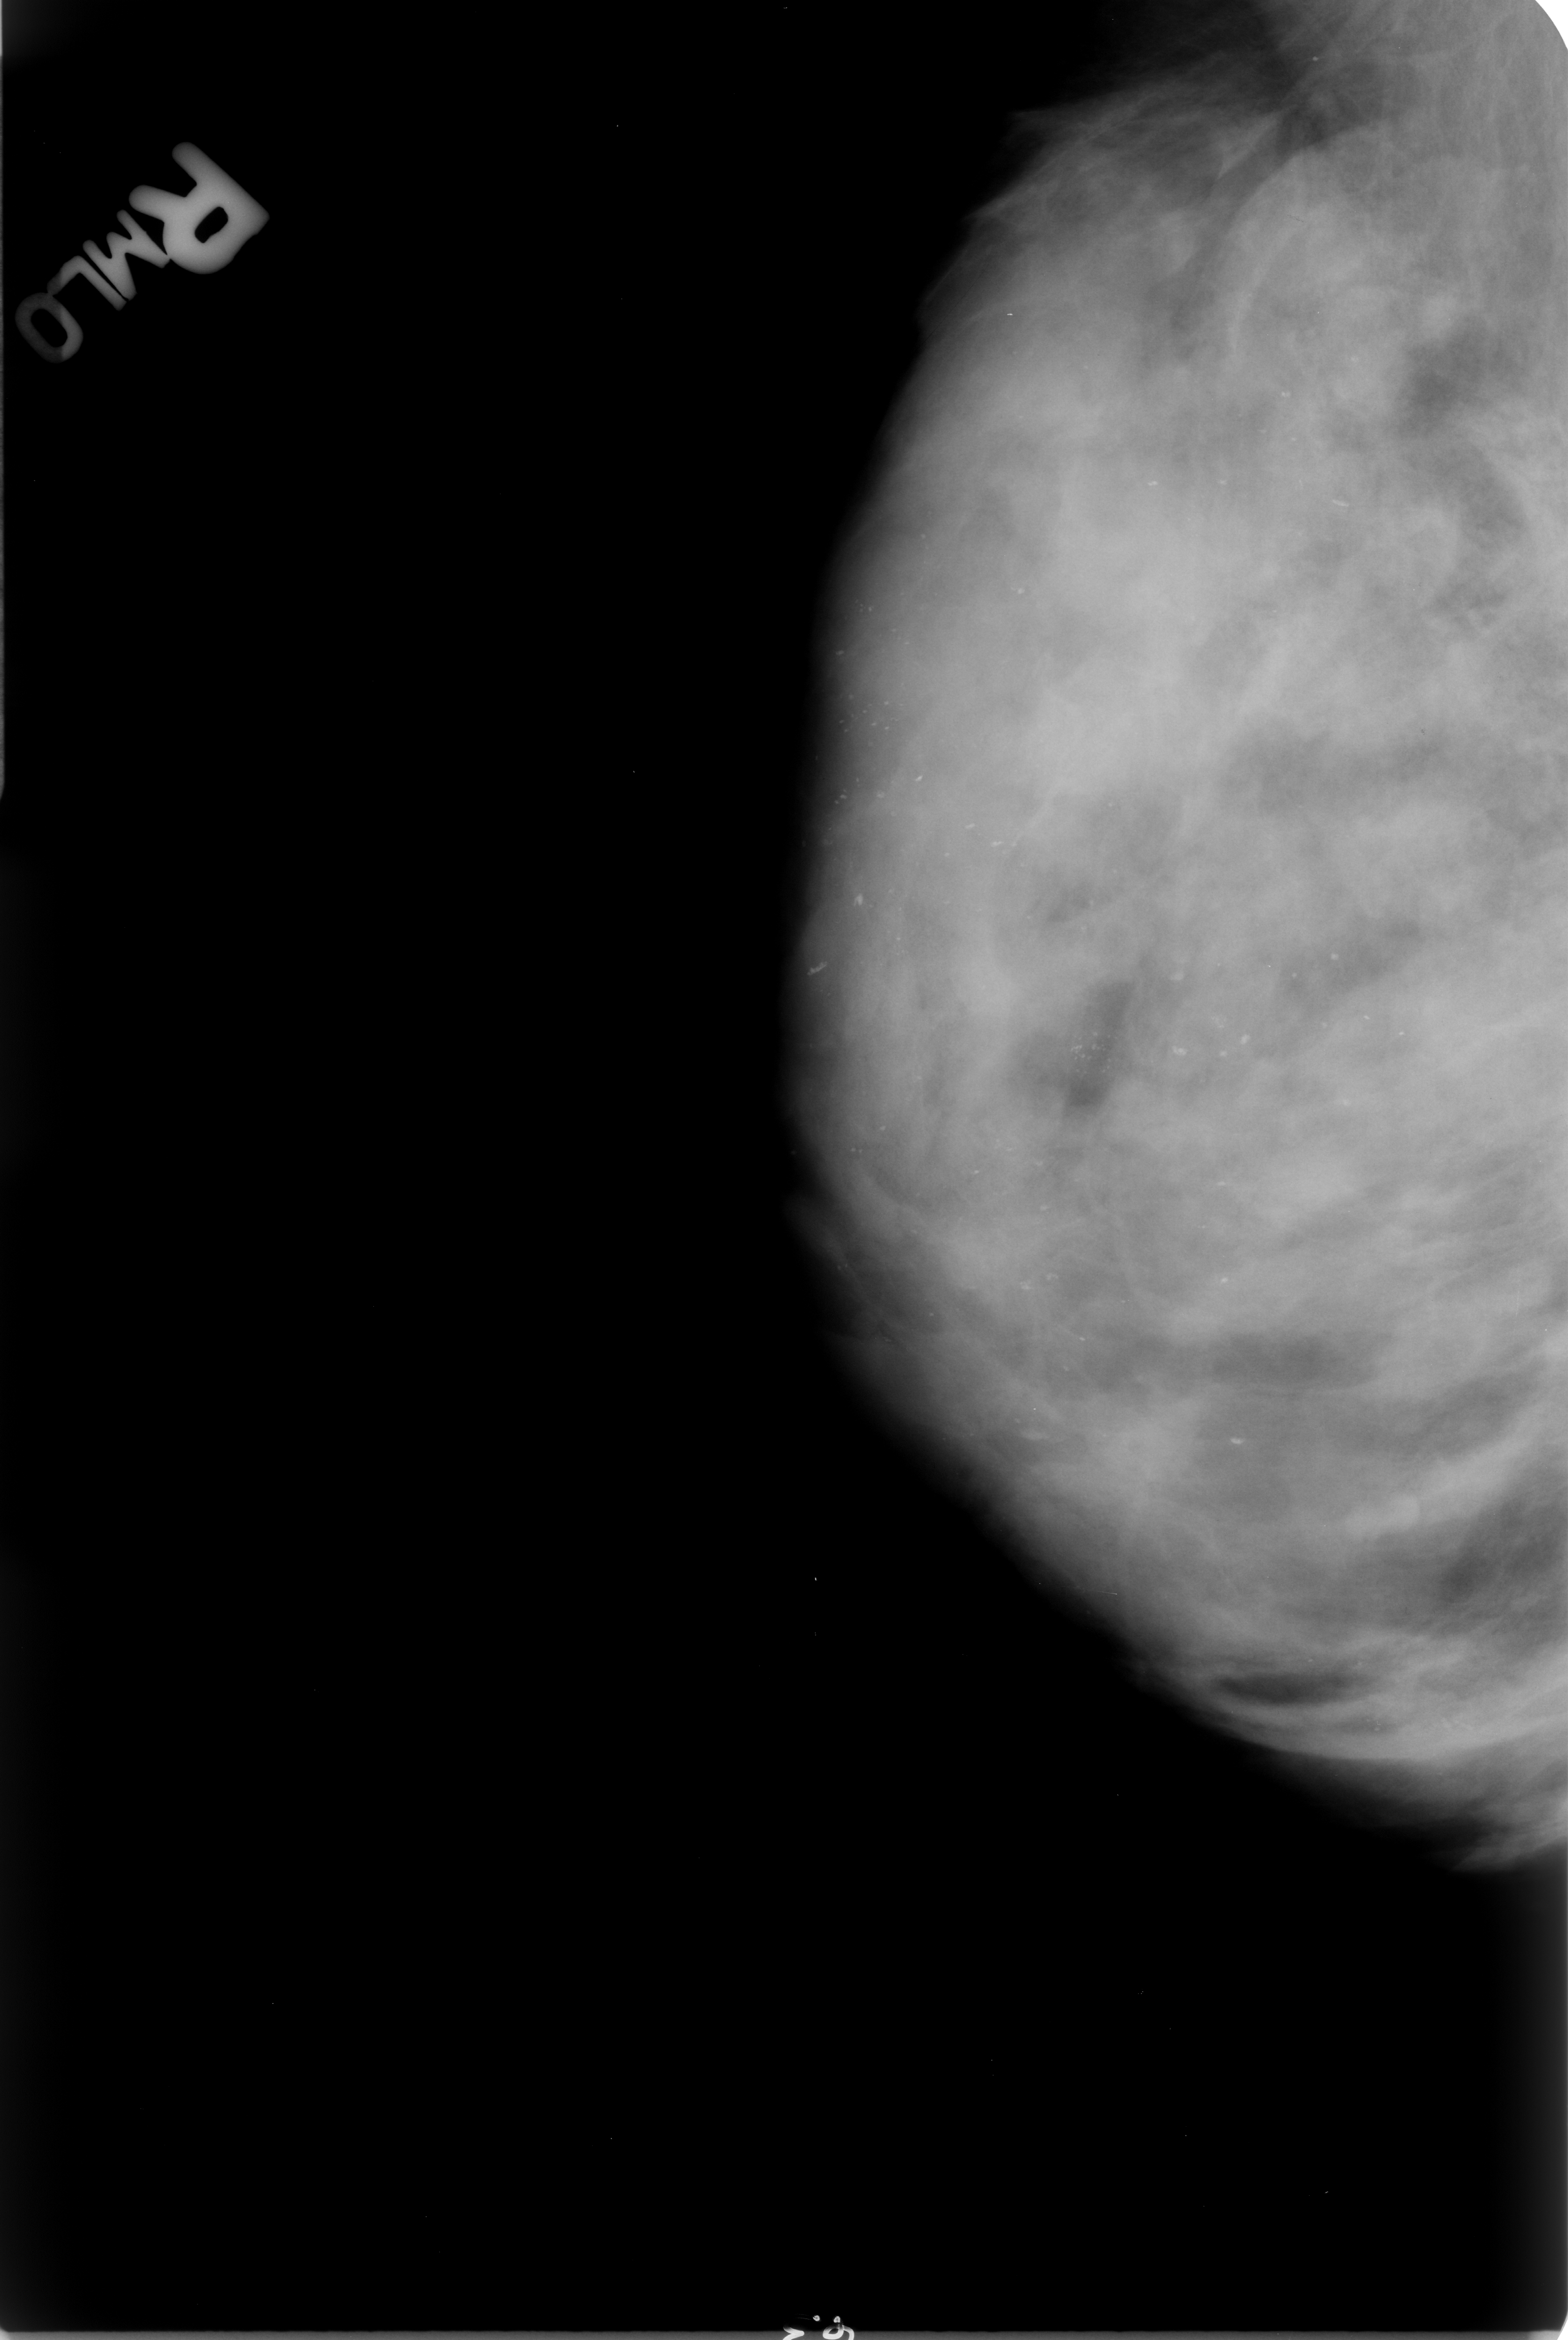
Mammogram (digitized film), right breast, mediolateral oblique (MLO) view.
- Radiologist-marked abnormalities on this image: calcifications, morphology punctate / pleomorphic, distribution clustered; BI-RADS assessment category 4; subtlety rating 2 on a 1 (subtle) to 5 (obvious) scale; pathology result (as recorded, not read from the image): benign.